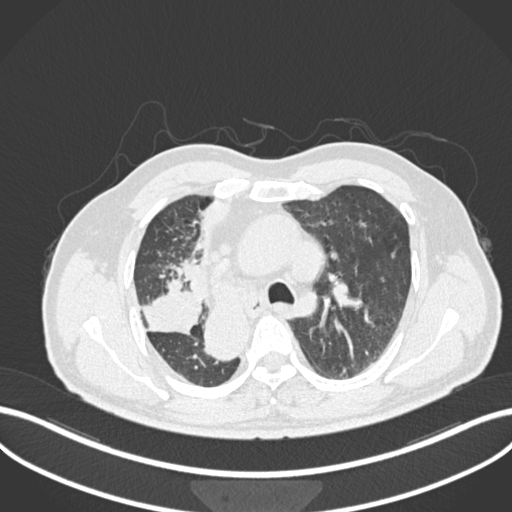
Chest CT, one axial slice. Slice 162 of 206 in the series (ordered by position). Reconstruction kernel B30f. 120 kVp. Lung window (W 1500 / L -600 HU). 512 × 512 image matrix, field of view 400 × 400 mm. Male patient, age 67 years. Case-level facts recorded for this patient, not image findings: clinical TNM (as recorded): T2a N0 M0.
Annotated regions visible in this slice (rectangle marked by the reading radiologist):
- lung tumour (recorded histology: squamous cell carcinoma): bounding box (x1, y1, x2, y2) in pixels: (137, 274, 202, 339)